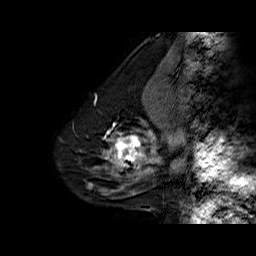
Breast MRI (dynamic contrast-enhanced), one sagittal slice. Slice 17 of 60 in the series (ordered by position). Dynamic contrast-enhanced series, time point 2 of 6 at this slice position (early post-contrast). 1.5 T. TE 6.3 ms, TR 32.5 ms. 256 × 256 image matrix. Female patient. Case-level facts recorded for this patient, not image findings: setting: breast cancer imaged before/during neoadjuvant chemotherapy; receptor status: triple-negative.
Outlined on this slice (semi-automatically segmented with operator editing):
- analysis volume of interest (the breast-tissue region the enhancement analysis was run in; not a lesion): box from (x=108, y=129) to (x=154, y=177) px
- tumour enhancement mask (voxels above the 100 % enhancement threshold inside the analysis volume of interest): (x=108, y=132)–(x=154, y=169)